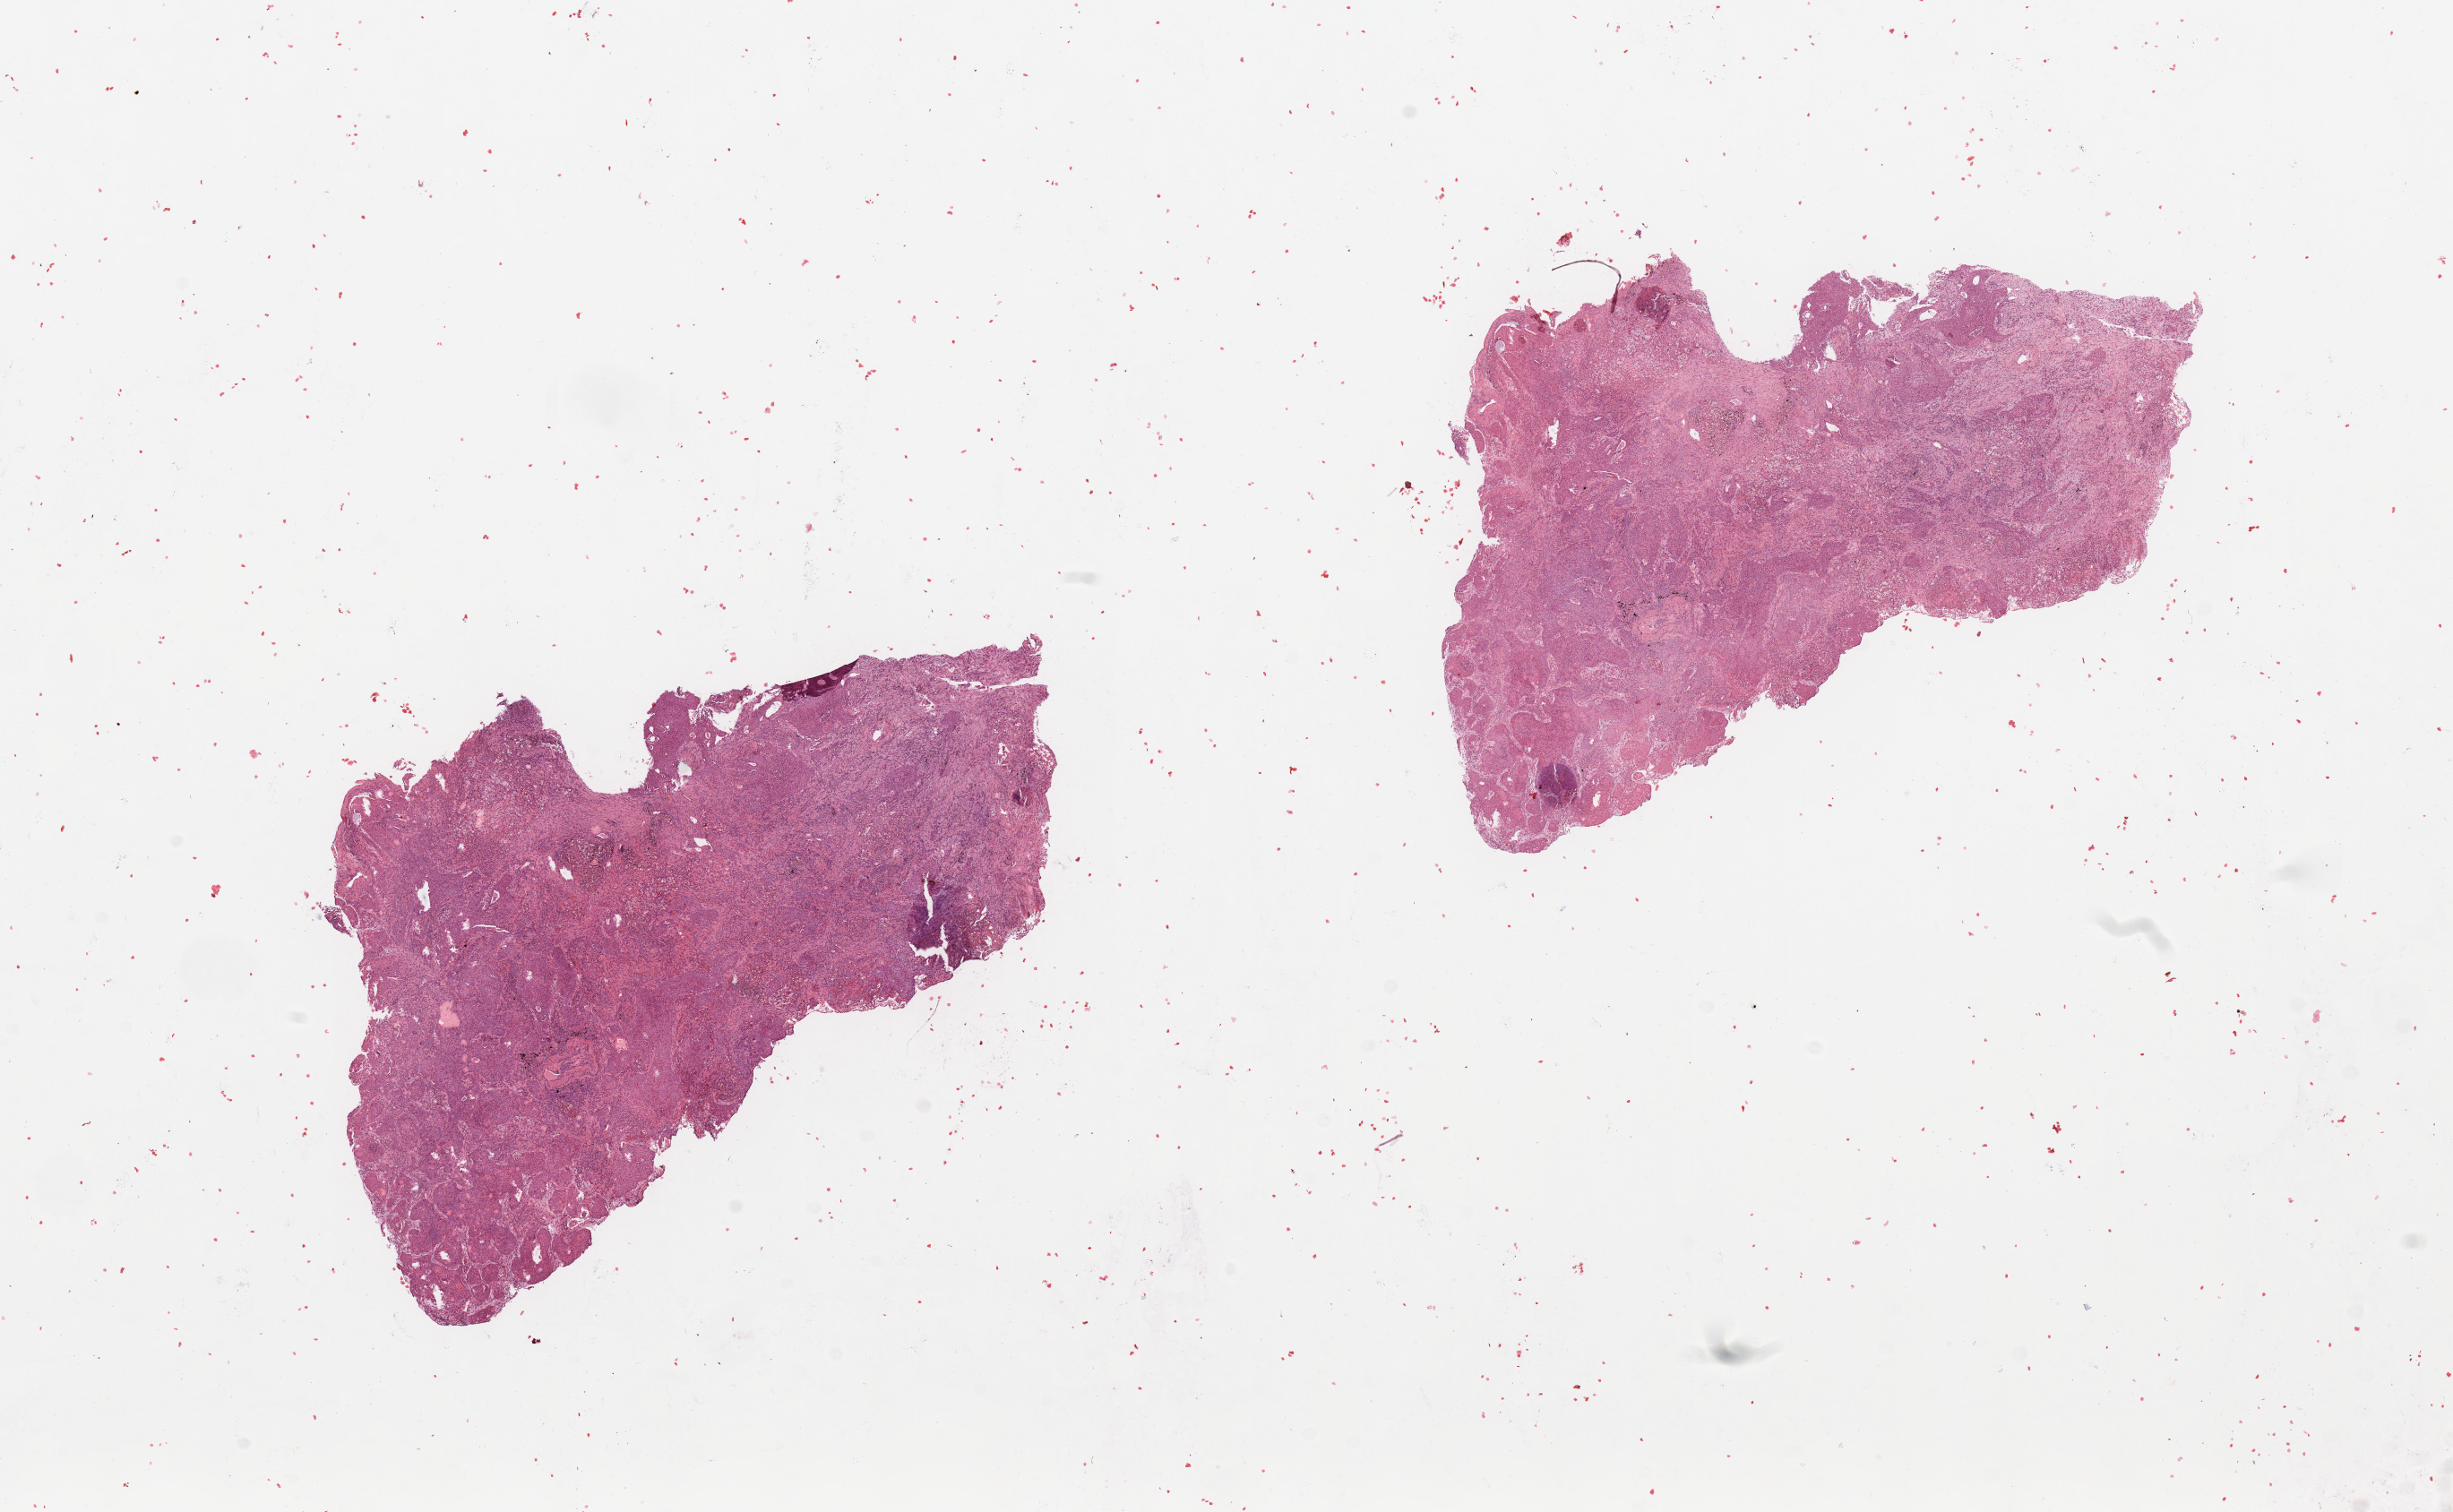
Whole-slide histology image, H&E — a low-resolution overview of the entire scanned area, about 21.7 x 13.4 mm (slide scanned at 20x), tumour tissue sample, sampled site: lung. Male, 77 y/o.
Diagnosis: Squamous cell carcinoma, NOS.